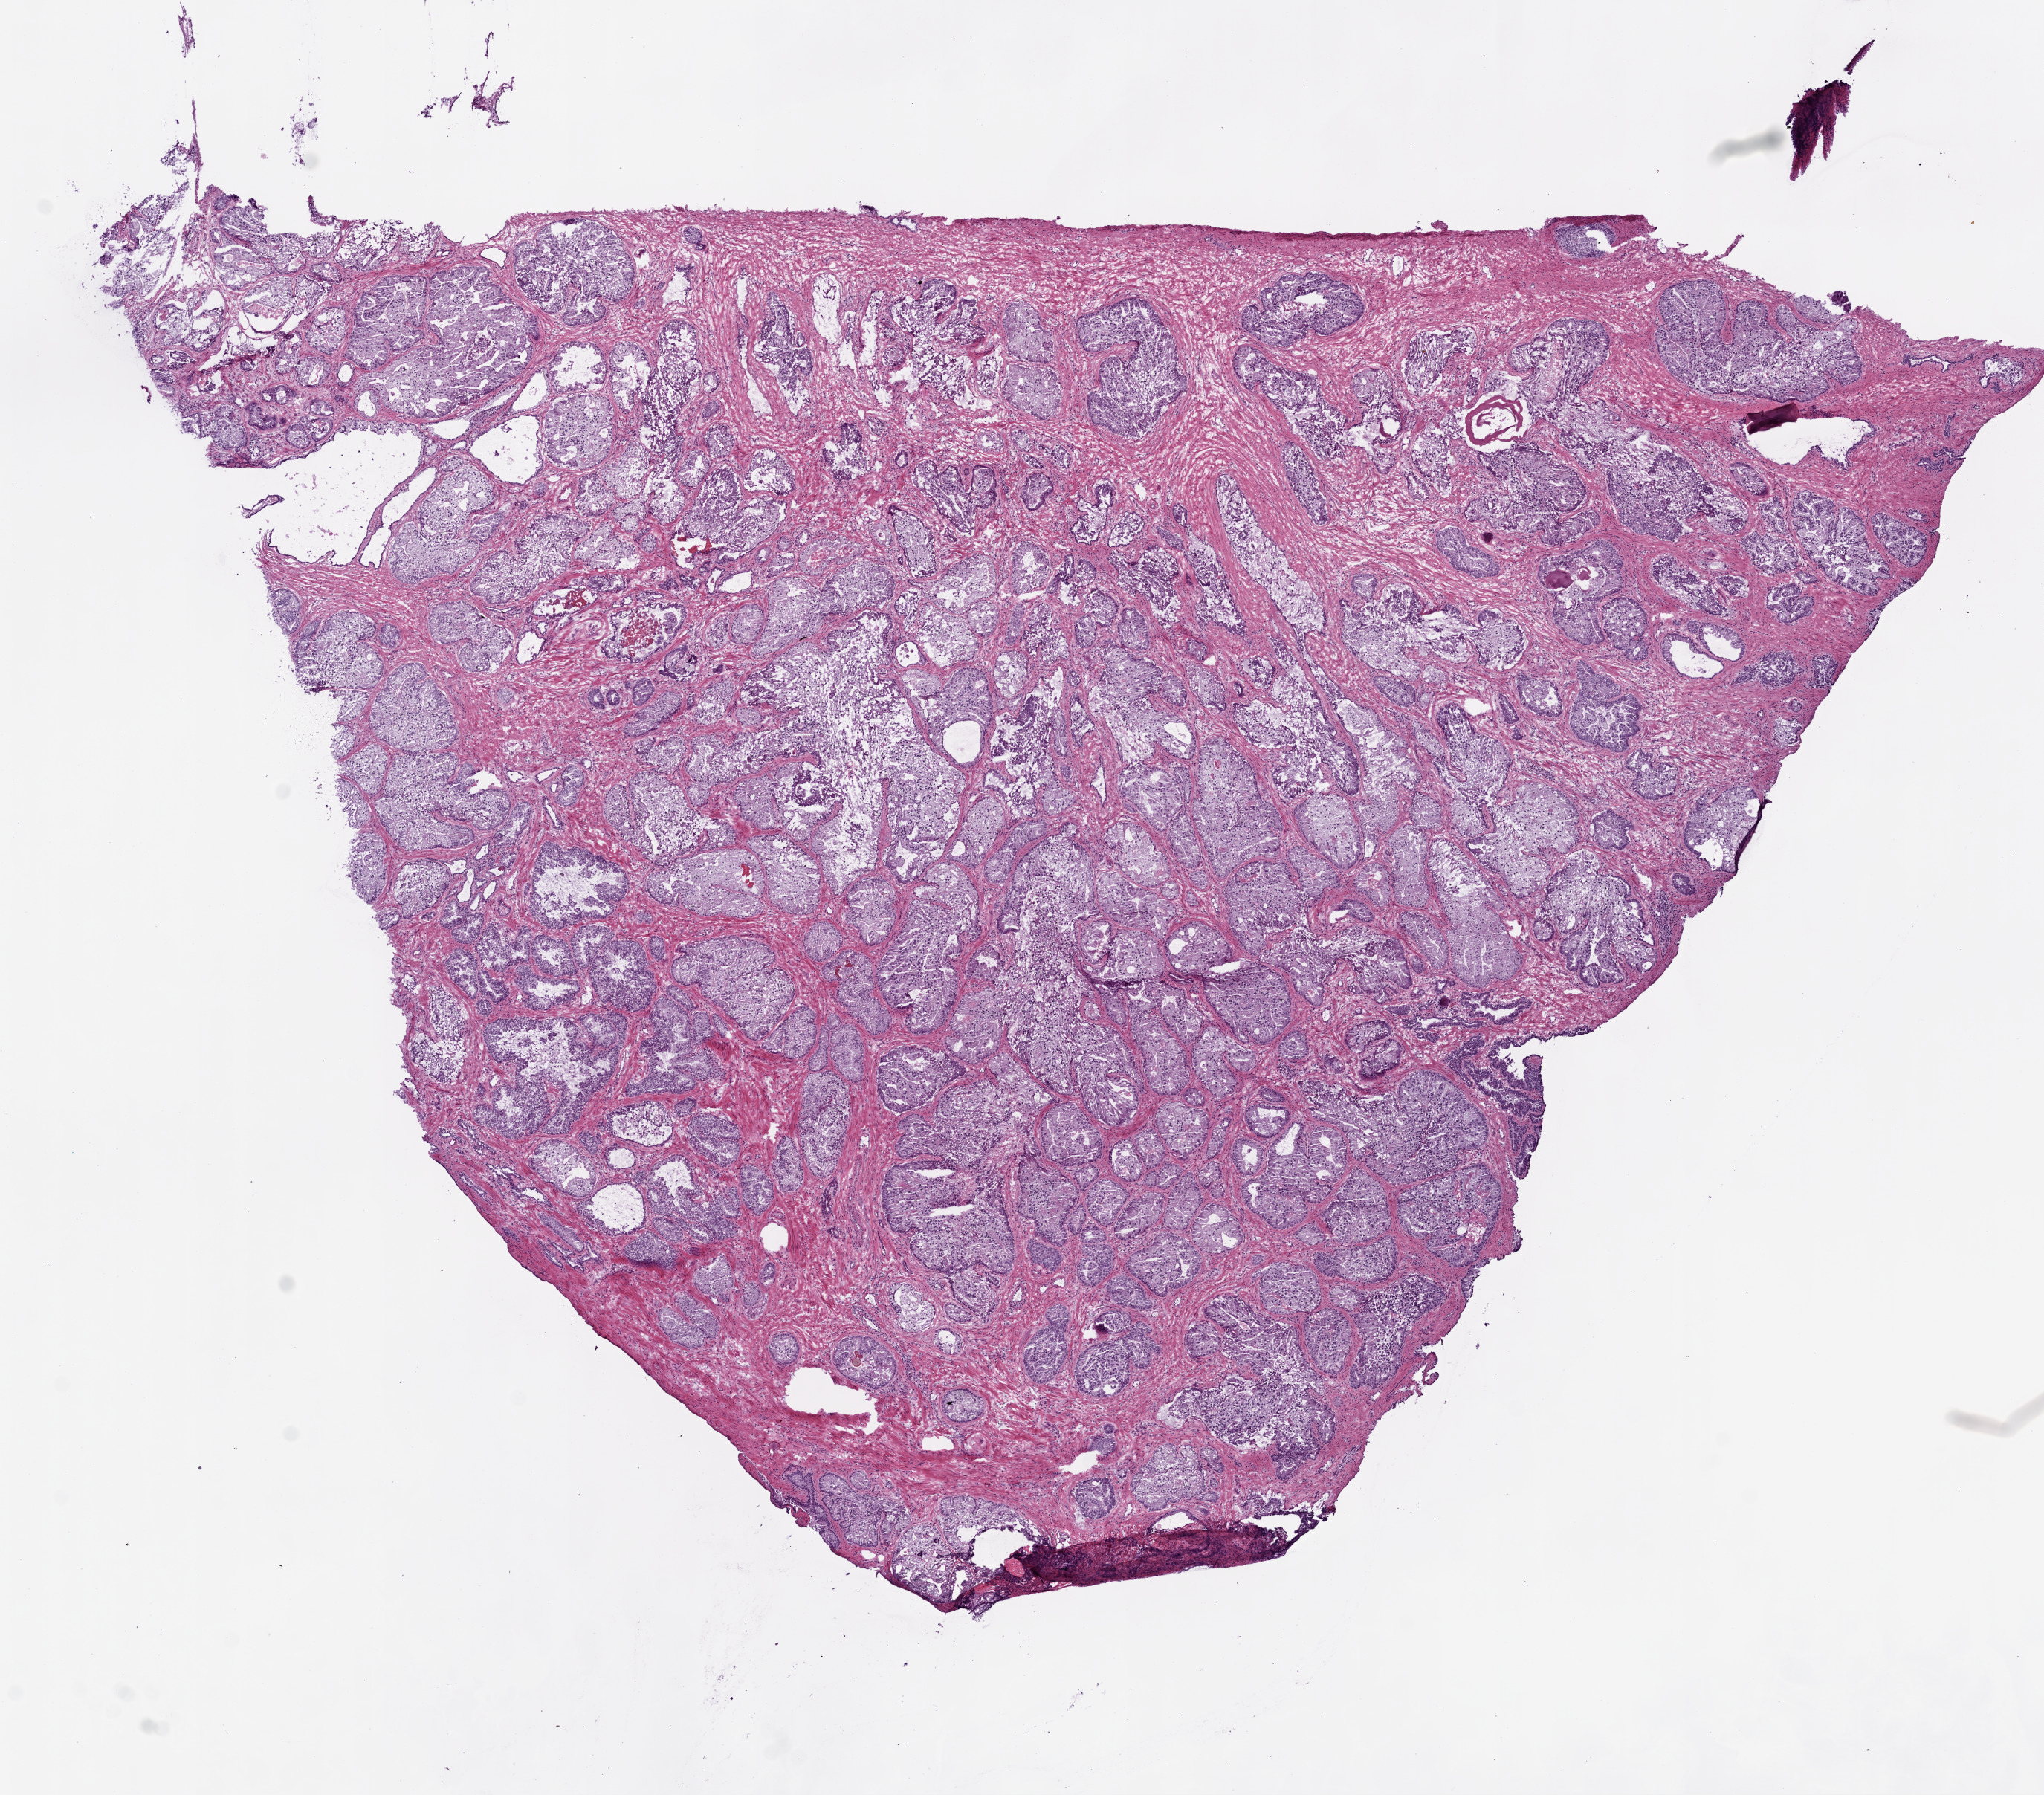
Whole-slide histology image, H&E — shown as a low-resolution overview of the whole scanned area (about 11.0 x 9.7 mm, acquisition: 20x scan); frozen section from the top of the tissue portion; sample: primary tumour, prostate. Male, age 63 years at initial diagnosis. Gleason score: 7 (3+4). Composition of this section per pathologist review: tumour cells 50%, tumour nuclei 60%, normal cells 20%, stromal cells 28%, necrosis 2%. Inflammatory infiltration, as recorded: lymphocyte infiltration 3%, monocyte infiltration 0%, neutrophil infiltration 0%.
* lymph nodes positive (case pathology): 0 of 2 examined
* laterality: right
* pathologic diagnosis: Acinar cell carcinoma (prostate gland)